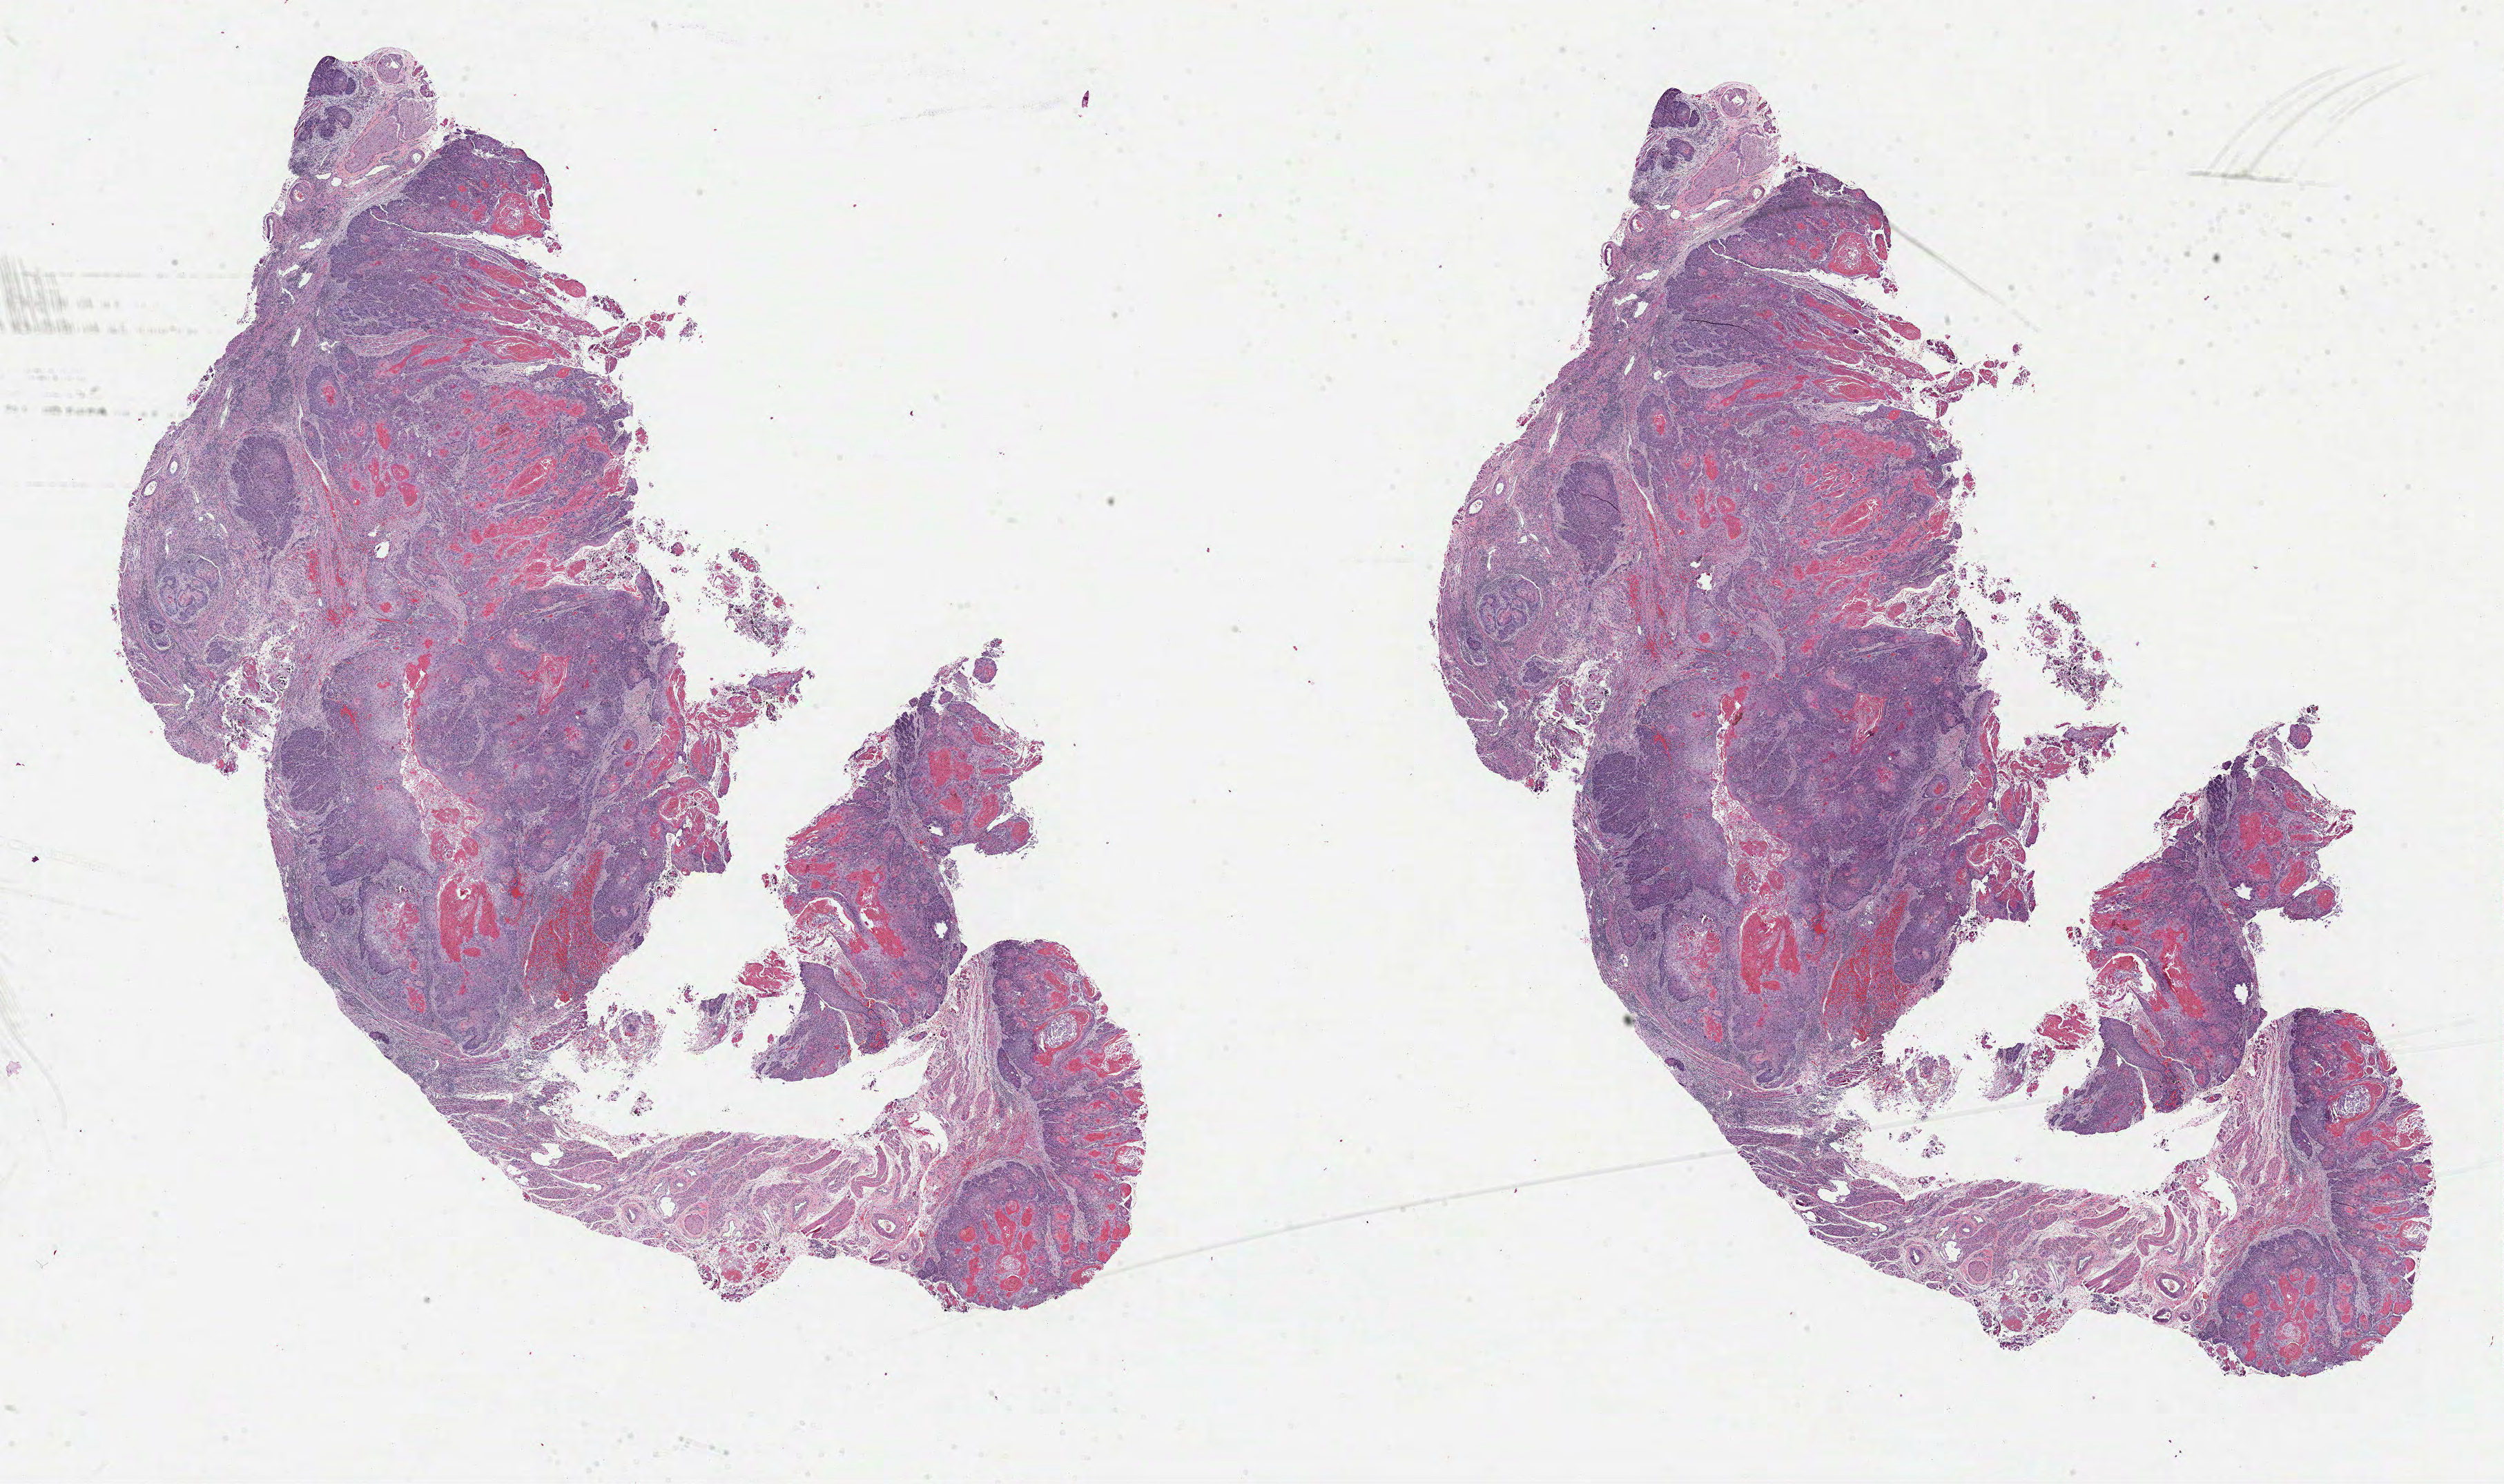
Whole-slide histology image, H&E-stained — low-resolution overview of the scanned area, about 29.2 x 17.3 mm (from a 40x scan), formalin-fixed paraffin-embedded (FFPE) diagnostic section, head and neck, primary tumour sample. Patient: male, age at initial diagnosis 19 years. Histologic grade: G2 (moderately differentiated).
- TNM: T2 N2b
- AJCC pathologic stage: IVA (7th edition)
- diagnosis: Squamous cell carcinoma, NOS (tongue, NOS)